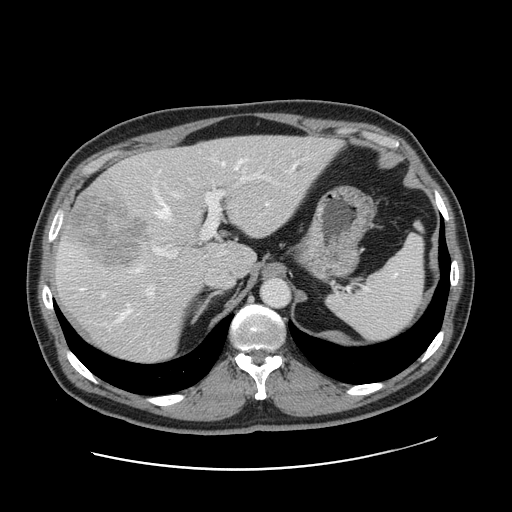
Contrast-enhanced abdominal CT, one axial slice. Position 115 of 178 along the scan axis. Intravenous contrast given. Soft-tissue window (W 400 / L 40 HU). 2.5 mm slice thickness. 512 × 512 image matrix. Male patient, age 63 years. From the clinical record (not read from this slice): diagnosis: colorectal cancer liver metastases, imaged before liver resection; multiple liver metastases: yes; largest metastasis: 8 cm; disease in both lobes: yes.
Outlined on this slice (outlined manually by an expert reader):
- hepatic veins: box from (x=81, y=161) to (x=295, y=320) px
- liver: (x=54, y=137)–(x=338, y=364)
- planned liver remnant (the part of the liver to remain after resection): (x=137, y=137)–(x=338, y=276)
- portal vein (with intrahepatic branches): (x=147, y=171)–(x=270, y=295)
- liver metastasis: (x=297, y=166)–(x=303, y=172)
- liver metastasis: (x=68, y=194)–(x=151, y=266)